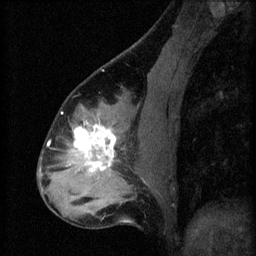
Breast MRI (dynamic contrast-enhanced), one sagittal slice. Position 26 of 60 along the scan axis. 3 images stored at this slice position (order not interpretable as contrast timing). 1.5 T. TE 4.2 ms, TR 8.2 ms. 2.3 mm slice thickness. 256 × 256 image matrix, field of view 180 × 180 mm. Female patient, age 37 years.
Structures marked on this image (semi-automatic segmentation, software-assisted and operator-edited):
- analysis volume of interest (the breast-tissue region the enhancement analysis was run in; not a lesion): bounding box <67,120,122,179> (left, top, right, bottom; pixels)
- tumour enhancement mask (voxels above the 70 % enhancement threshold inside the analysis volume of interest): <71,120,116,173>